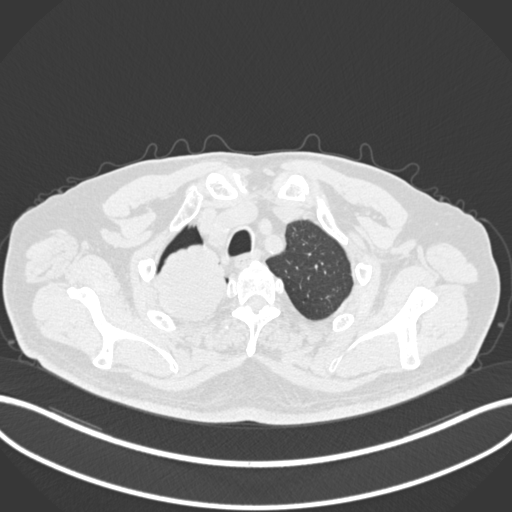
Chest CT, one axial slice. Position 186 of 218 along the scan axis. Reconstruction kernel B30f. 120 kVp. Lung window (W 1500 / L -600 HU). 1 mm slice thickness. 512 × 512 image matrix. Male patient, age 68 years. Case-level facts recorded for this patient, not image findings: clinical TNM (as recorded): T2a N0 M0.
Outlined on this slice (bounding box drawn by a radiologist):
- lung tumour (recorded histology: adenocarcinoma): bounding box [x1, y1, x2, y2] px = [150, 236, 232, 324]